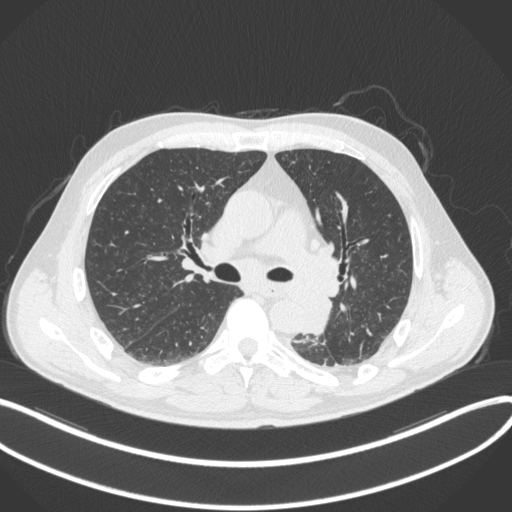
Chest CT, one axial slice. Slice 209 of 328 in the series (ordered by position). Reconstruction kernel B31f. 120 kVp. Lung window (W 1500 / L -600 HU). 512 × 512 image matrix. Male patient, age 59 years. From the clinical record (not read from this slice): clinical TNM (as recorded): T2a N2 M0.
Outlined on this slice (rectangle marked by the reading radiologist):
- lung tumour (recorded histology: squamous cell carcinoma): bounding box [x1, y1, x2, y2] px = [304, 286, 332, 338]